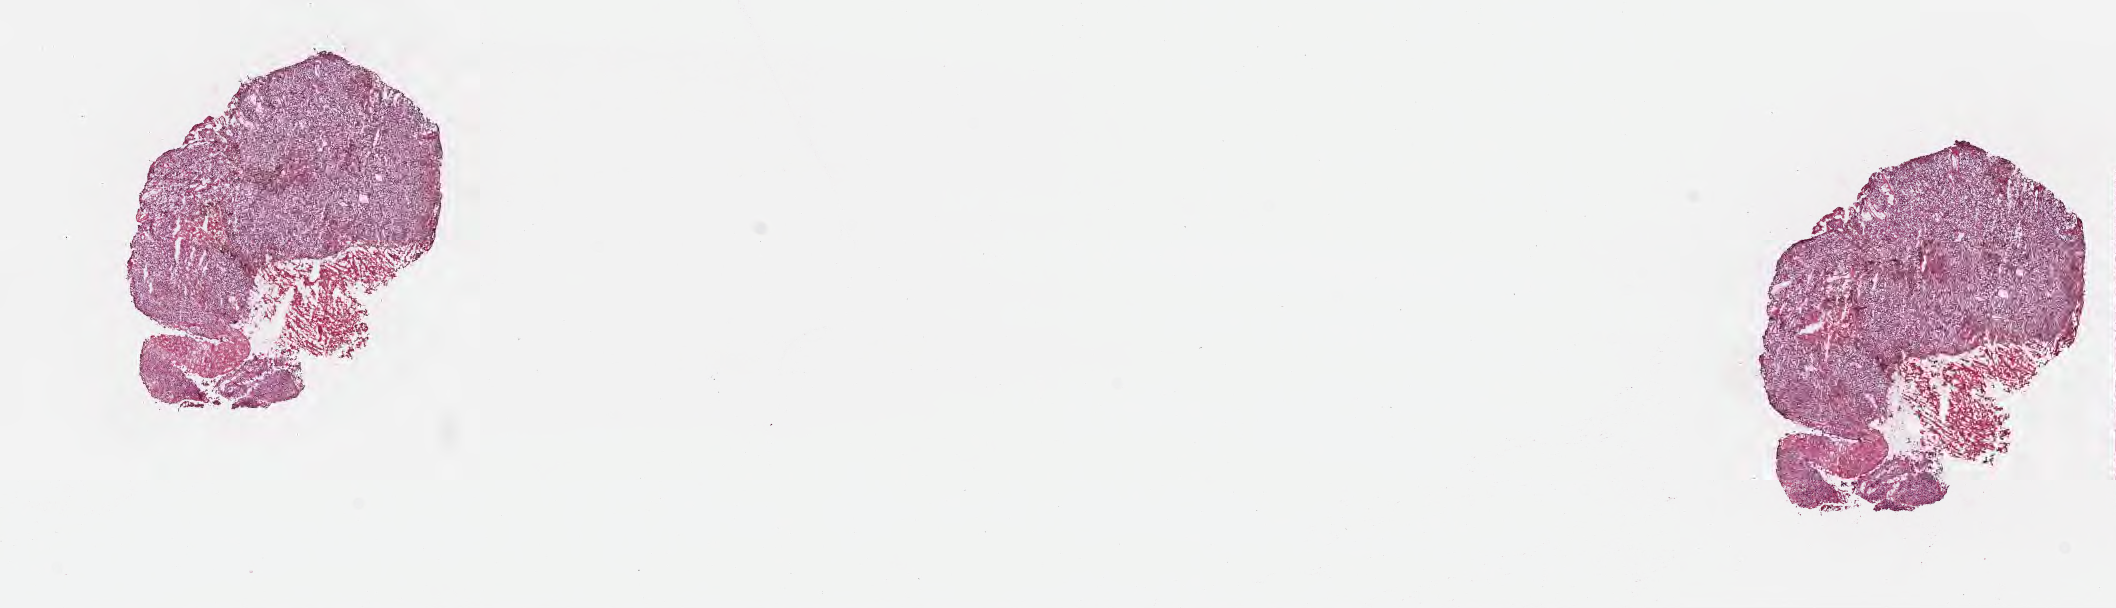
Digitized hematoxylin and eosin (H&E)-stained section — shown as a low-resolution overview of the whole scanned area (about 17.1 x 4.9 mm); frozen section (tissue freezing medium); metastatic tumor tissue, resected from brain. Patient: female, age at initial diagnosis 60 years. Pathologist review of this section (percent, as recorded): tumor cells 70%, tumor nuclei 80%, stromal cells 10%, necrosis 20%, normal cells 0%. Infiltration values recorded for this section: lymphocyte infiltration 0%, monocyte infiltration 0%, neutrophil infiltration 0%.
Patient diagnosis (primary): Malignant melanoma, NOS. Section: top of the tissue portion.